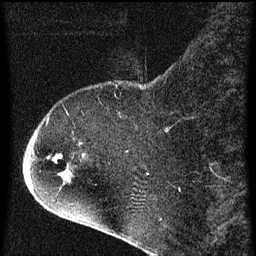
Breast MRI (dynamic contrast-enhanced), one sagittal slice; slice 17 of 60 in the series (ordered by position); dynamic contrast-enhanced series, image 2 of 4 at this slice position (ordered by acquisition); 1.5 T; TE 4.2 ms, TR 8 ms; 2 mm slice thickness; 256 × 256 image matrix, field of view 180 × 180 mm. Patient: female, 71 years.
Structures marked on this image (semi-automatic segmentation, software-assisted and operator-edited):
- analysis volume of interest (the breast-tissue region the enhancement analysis was run in; not a lesion): bounding box (x1, y1, x2, y2) in pixels: (32, 86, 141, 205)
- tumour enhancement mask (voxels above the 70 % enhancement threshold inside the analysis volume of interest): (53, 154, 83, 163)